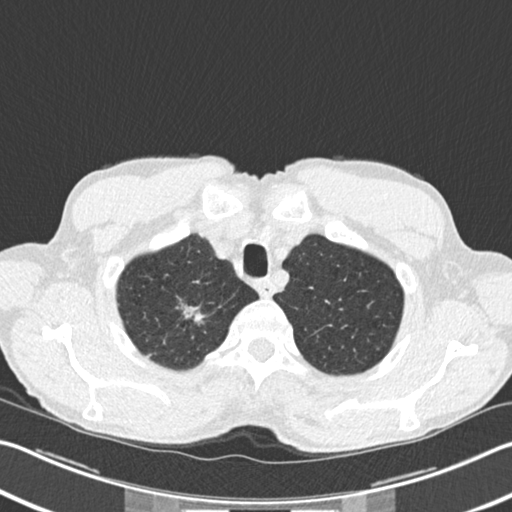
Axial slice from a low-dose chest CT screening exam. Second screening round (one year after baseline). Lung window (W 1500 / L -600 HU). 2 mm slice thickness. Standard (soft-tissue) reconstruction kernel (B30f). 120 kVp. Slice 27 of 220 in the series. 512 × 512 image matrix. Male participant, aged 62 years at enrolment. Former smoker at enrolment.
• Lesion marked by an expert reader, bounding box [x1, y1, x2, y2] px = [168, 296, 210, 342].
• The screening reader recorded 2 non-calcified nodules or masses ≥4 mm on this exam (right upper lobe, right upper lobe); which of them this box marks is not recorded.
• Lung cancer was diagnosed 5 days after this screen: bronchiolo-alveolar adenocarcinoma, NOS, right upper lobe, well differentiated (G1), stage IA (AJCC 6th edition), 15 mm at pathology.